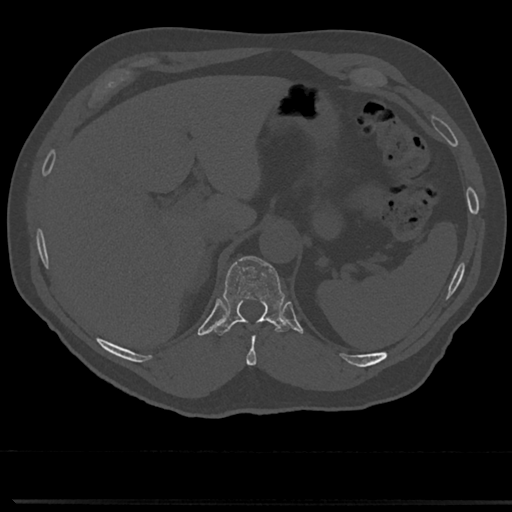
CT including the spine, one axial slice. Position 218 of 817 along the scan axis. Reconstruction kernel Br40s/3. Bone window (W 1800 / L 400 HU). 512 × 512 image matrix, field of view 355 × 355 mm. Patient: male, 61 years. From the clinical record (not read from this slice): primary cancer: prostate.
Outlined on this slice (semi-automatically segmented with operator editing):
- T10 vertebra: box from (x=245, y=321) to (x=274, y=366) px
- T11 vertebra: (x=218, y=256)–(x=285, y=334)